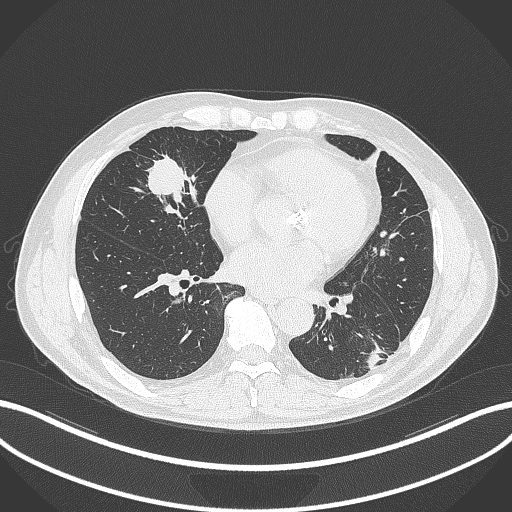
Chest CT, one axial slice. Position 120 of 399 along the scan axis. 120 kVp. Lung window (W 1500 / L -600 HU). 1 mm slice thickness. 512 × 512 image matrix, field of view 400 × 400 mm. Male patient, age 59 years. Case-level facts recorded for this patient, not image findings: clinical TNM (as recorded): T2a N1 M0.
Outlined on this slice (bounding box drawn by a radiologist):
- lung tumour (recorded histology: adenocarcinoma): bounding box <141,149,210,214> (left, top, right, bottom; pixels)